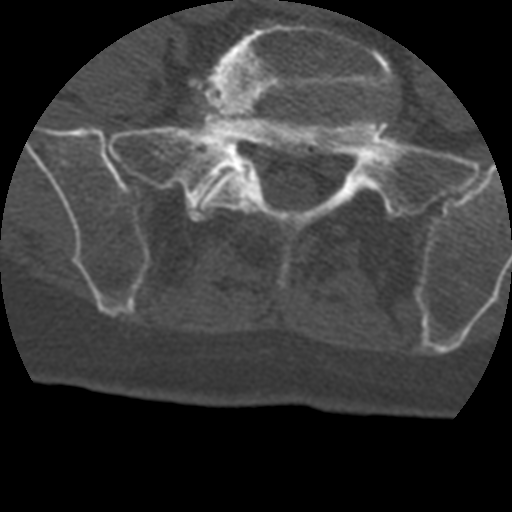
CT including the spine, one axial slice. Position 32 of 399 along the scan axis. Reconstruction kernel STANDARD. Bone window (W 1800 / L 400 HU). 1.25 mm slice thickness. 512 × 512 image matrix, field of view 160 × 160 mm. Patient age 69 years. Case-level facts recorded for this patient, not image findings: primary cancer: prostate.
Annotated regions visible in this slice (semi-automatic segmentation, software-assisted and operator-edited):
- L5 vertebra: bounding box [x1, y1, x2, y2] px = [199, 21, 395, 213]